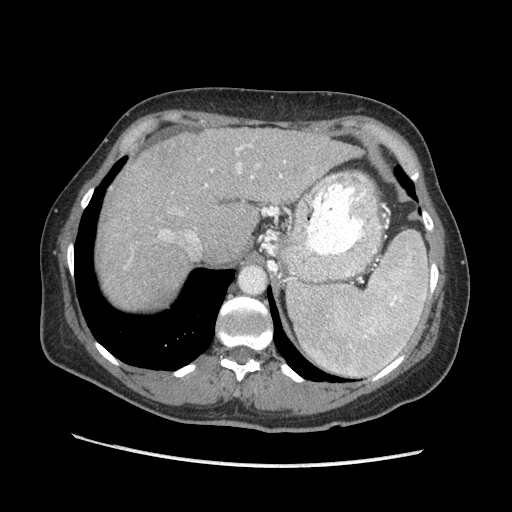
Contrast-enhanced abdominal CT (liver protocol), one axial slice. Position 145 of 170 along the scan axis. Reconstruction kernel STANDARD. 140 kVp. Soft-tissue window (W 400 / L 40 HU). 2.5 mm slice thickness. 512 × 512 image matrix. From the clinical record (not read from this slice): diagnosis: hepatocellular carcinoma (patient treated with transarterial chemoembolisation; whether this scan precedes or follows treatment is not stated here); TNM stage (as recorded): Stage-II; Child-Pugh class: A; tumour differentiation: no biopsy; tumour nodularity: multinodular.
Structures marked on this image (semi-automatic segmentation, software-assisted and operator-edited):
- abdominal aorta: bounding box <239,266,265,293> (left, top, right, bottom; pixels)
- liver parenchyma outside the tumour (the mass and vessels are separate outlines, so this box may not span the whole liver): <100,128,360,308>
- liver vessels: <129,144,286,262>